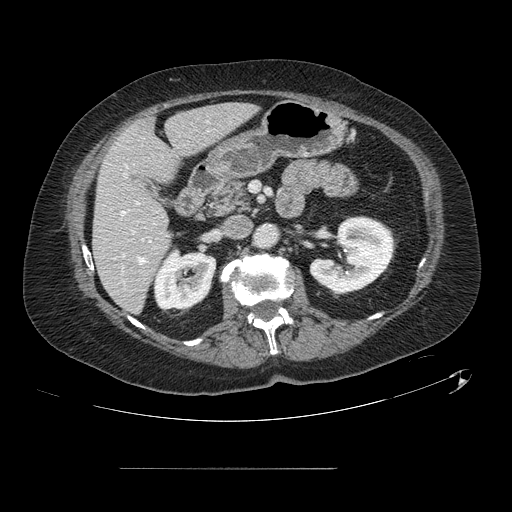
Contrast-enhanced abdominal CT, one axial slice. Slice 53 of 148 in the series (ordered by position). 120 kVp. Intravenous contrast given. Soft-tissue window (W 400 / L 40 HU). 2.5 mm slice thickness. 512 × 512 image matrix, field of view 439 × 439 mm. Female patient, age 75 years. From the clinical record (not read from this slice): diagnosis: colorectal cancer liver metastases, imaged before liver resection; multiple liver metastases: no; largest metastasis: 2.4 cm; disease in both lobes: no.
Outlined on this slice (expert manual segmentation):
- hepatic veins: bounding box (x1, y1, x2, y2) in pixels: (121, 174, 145, 264)
- liver: (94, 103, 256, 312)
- planned liver remnant (the part of the liver to remain after resection): (94, 103, 256, 312)
- portal vein (with intrahepatic branches): (137, 202, 139, 204)